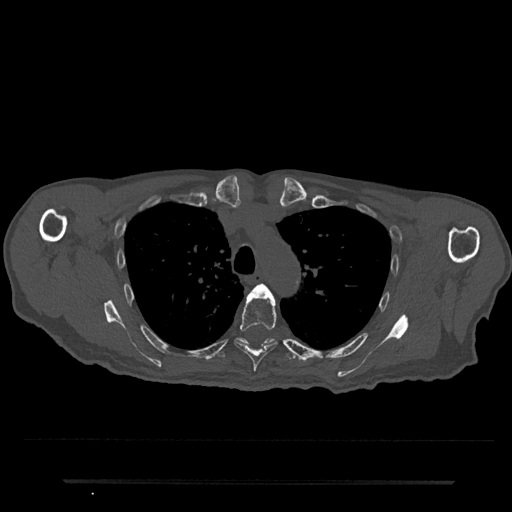
CT including the spine, one axial slice. Position 572 of 797 along the scan axis. Reconstruction kernel Br40s/3. 120 kVp. Bone window (W 1800 / L 400 HU). 512 × 512 image matrix, field of view 427 × 427 mm. Patient: male, 74 years. From the clinical record (not read from this slice): primary cancer: prostate.
Structures marked on this image (semi-automatic segmentation, software-assisted and operator-edited):
- T4 vertebra: box from (x=253, y=284) to (x=267, y=291) px
- T5 vertebra: (x=234, y=288)–(x=278, y=378)
- T6 vertebra: (x=215, y=337)–(x=297, y=360)